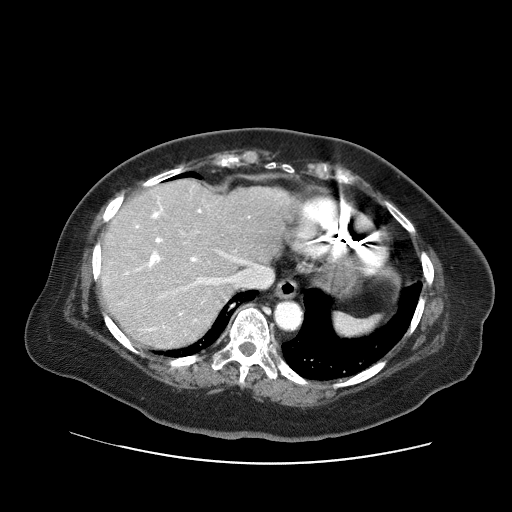
Contrast-enhanced abdominal CT (liver protocol), one axial slice; slice 50 of 71 in the series (ordered by position); reconstruction kernel STANDARD; 120 kVp; soft-tissue window (W 400 / L 40 HU); 2.5 mm slice thickness; 512 × 512 image matrix. Case-level facts recorded for this patient, not image findings: diagnosis: hepatocellular carcinoma (patient treated with transarterial chemoembolisation; whether this scan precedes or follows treatment is not stated here); TNM stage (as recorded): Stage-II; Child-Pugh class: A; tumour differentiation: poorly differentiated; tumour nodularity: multinodular.
Annotated regions visible in this slice (semi-automatic segmentation, software-assisted and operator-edited):
- liver parenchyma outside the tumour (the mass and vessels are separate outlines, so this box may not span the whole liver): box from (x=100, y=180) to (x=296, y=348) px
- liver vessels: (x=119, y=197)–(x=247, y=332)